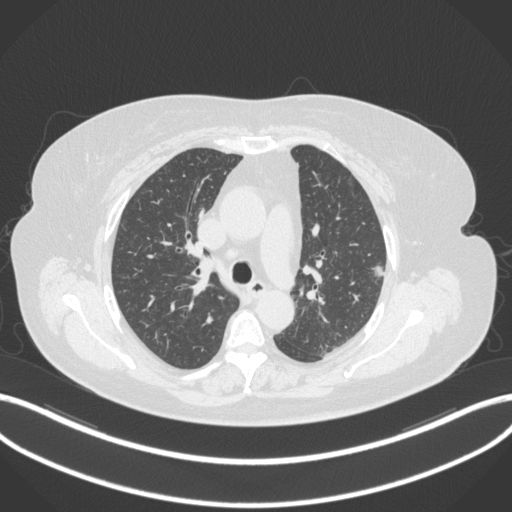
Chest CT, one axial slice. Position 215 of 310 along the scan axis. Reconstruction kernel B31f. 120 kVp. Lung window (W 1500 / L -600 HU). 512 × 512 image matrix. Patient: female, 70 years. Case-level facts recorded for this patient, not image findings: clinical TNM (as recorded): T1c N0 M0.
Outlined on this slice (rectangle marked by the reading radiologist):
- lung tumour (recorded histology: adenocarcinoma): bounding box [x1, y1, x2, y2] px = [370, 264, 387, 283]